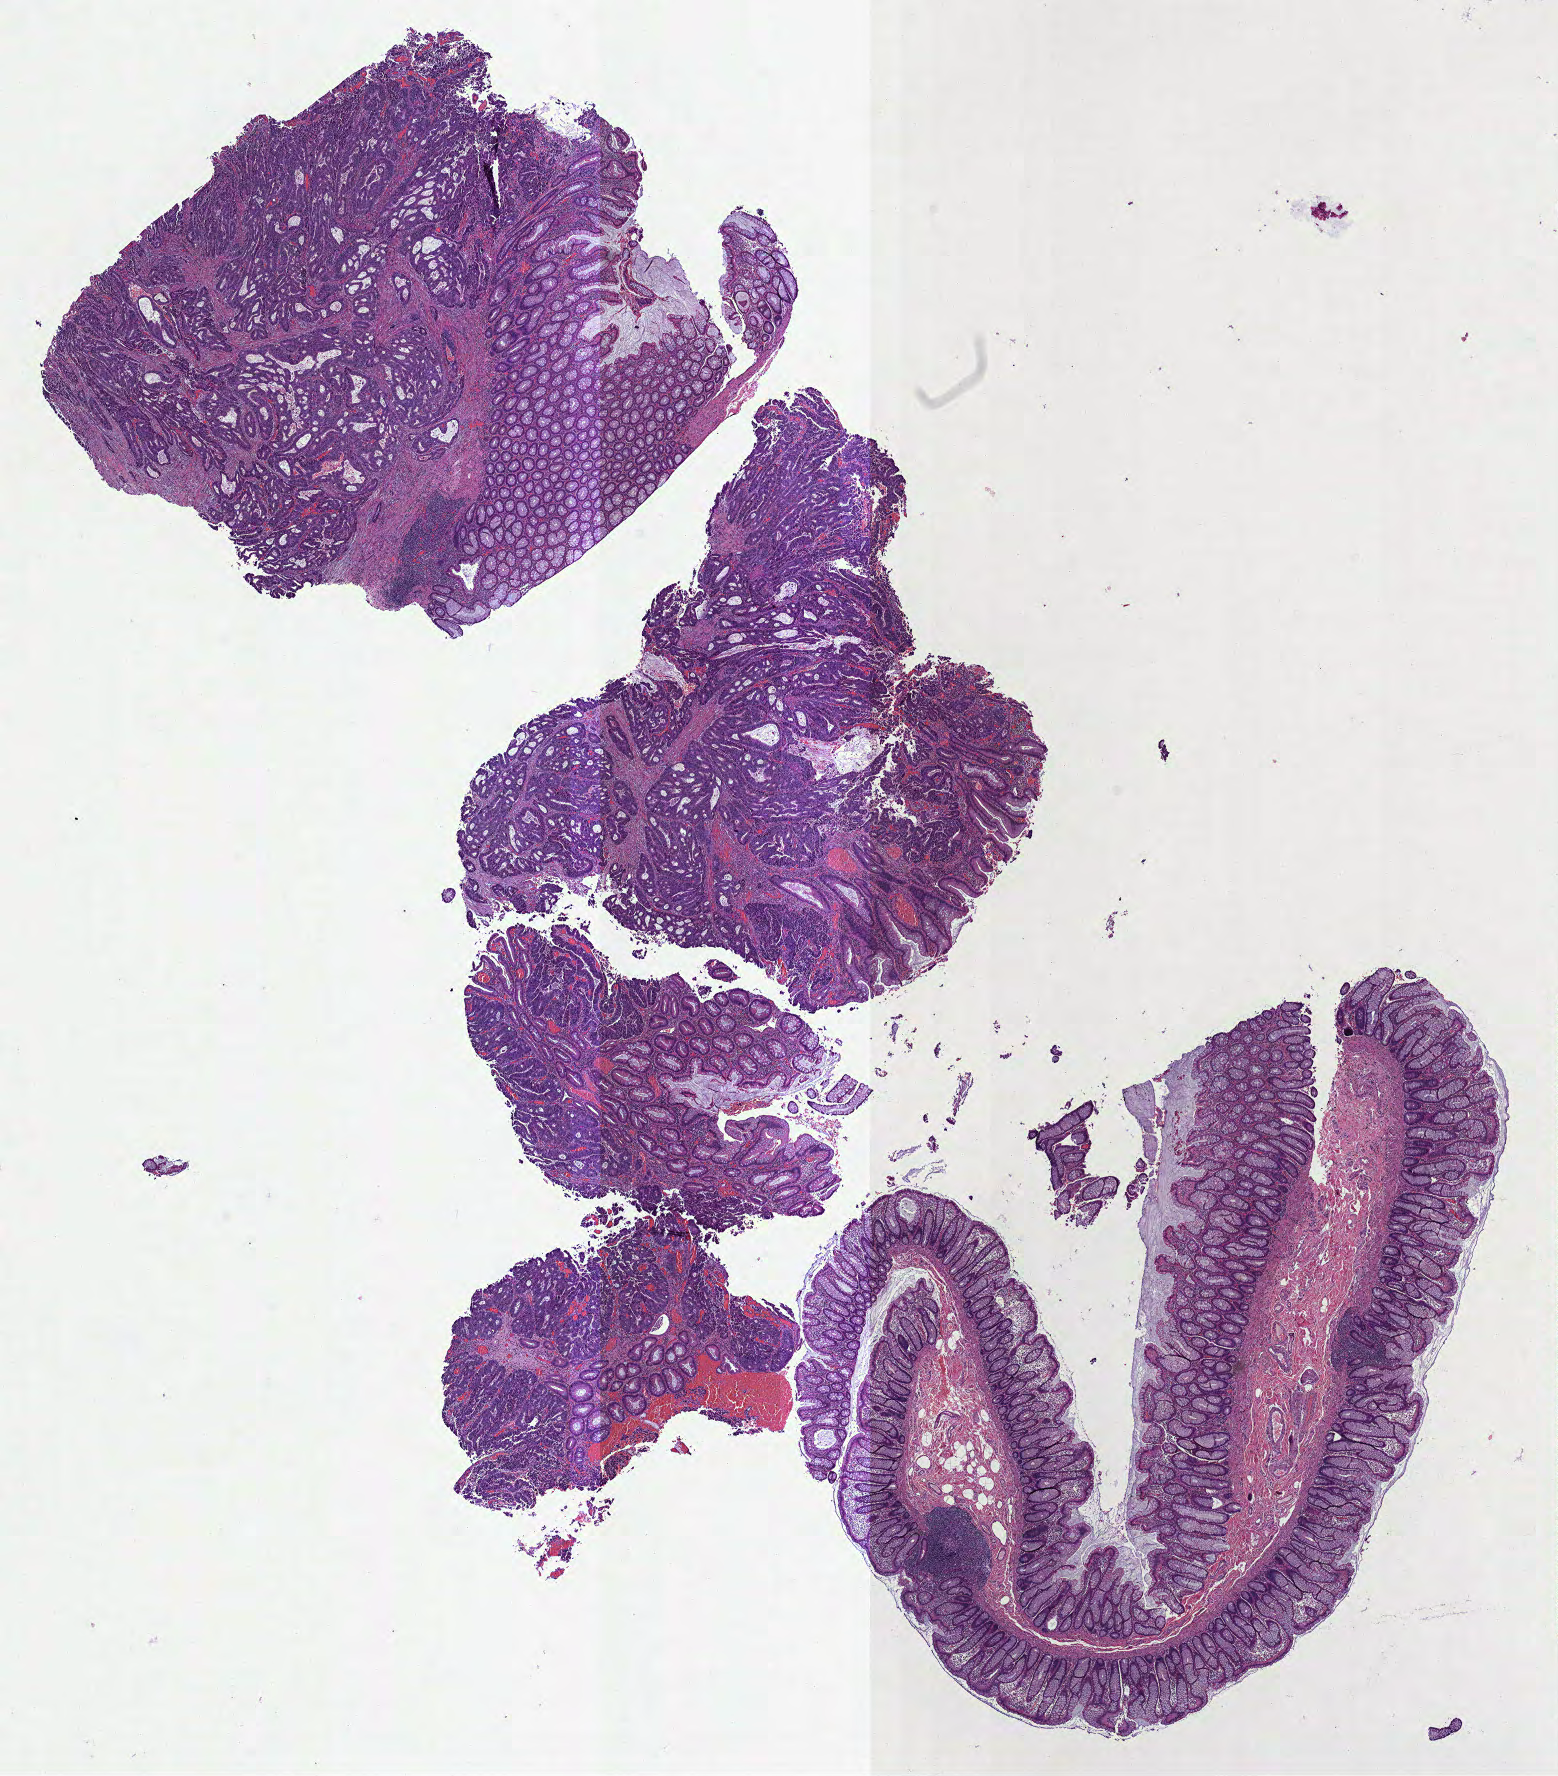
Hematoxylin and eosin (H&E) stained whole-slide image, shown as a low-resolution overview of the whole scanned area (about 12.6 x 14.3 mm, slide scanned at 40x), formalin-fixed paraffin-embedded (FFPE) diagnostic section, primary tumour sample from the colon. Patient: male, age at initial diagnosis 51 years.
AJCC pathologic stage: I (7th edition). Lymph nodes positive (case pathology): 0 of 11 examined. Pathologic diagnosis: Adenocarcinoma, NOS (ascending colon).